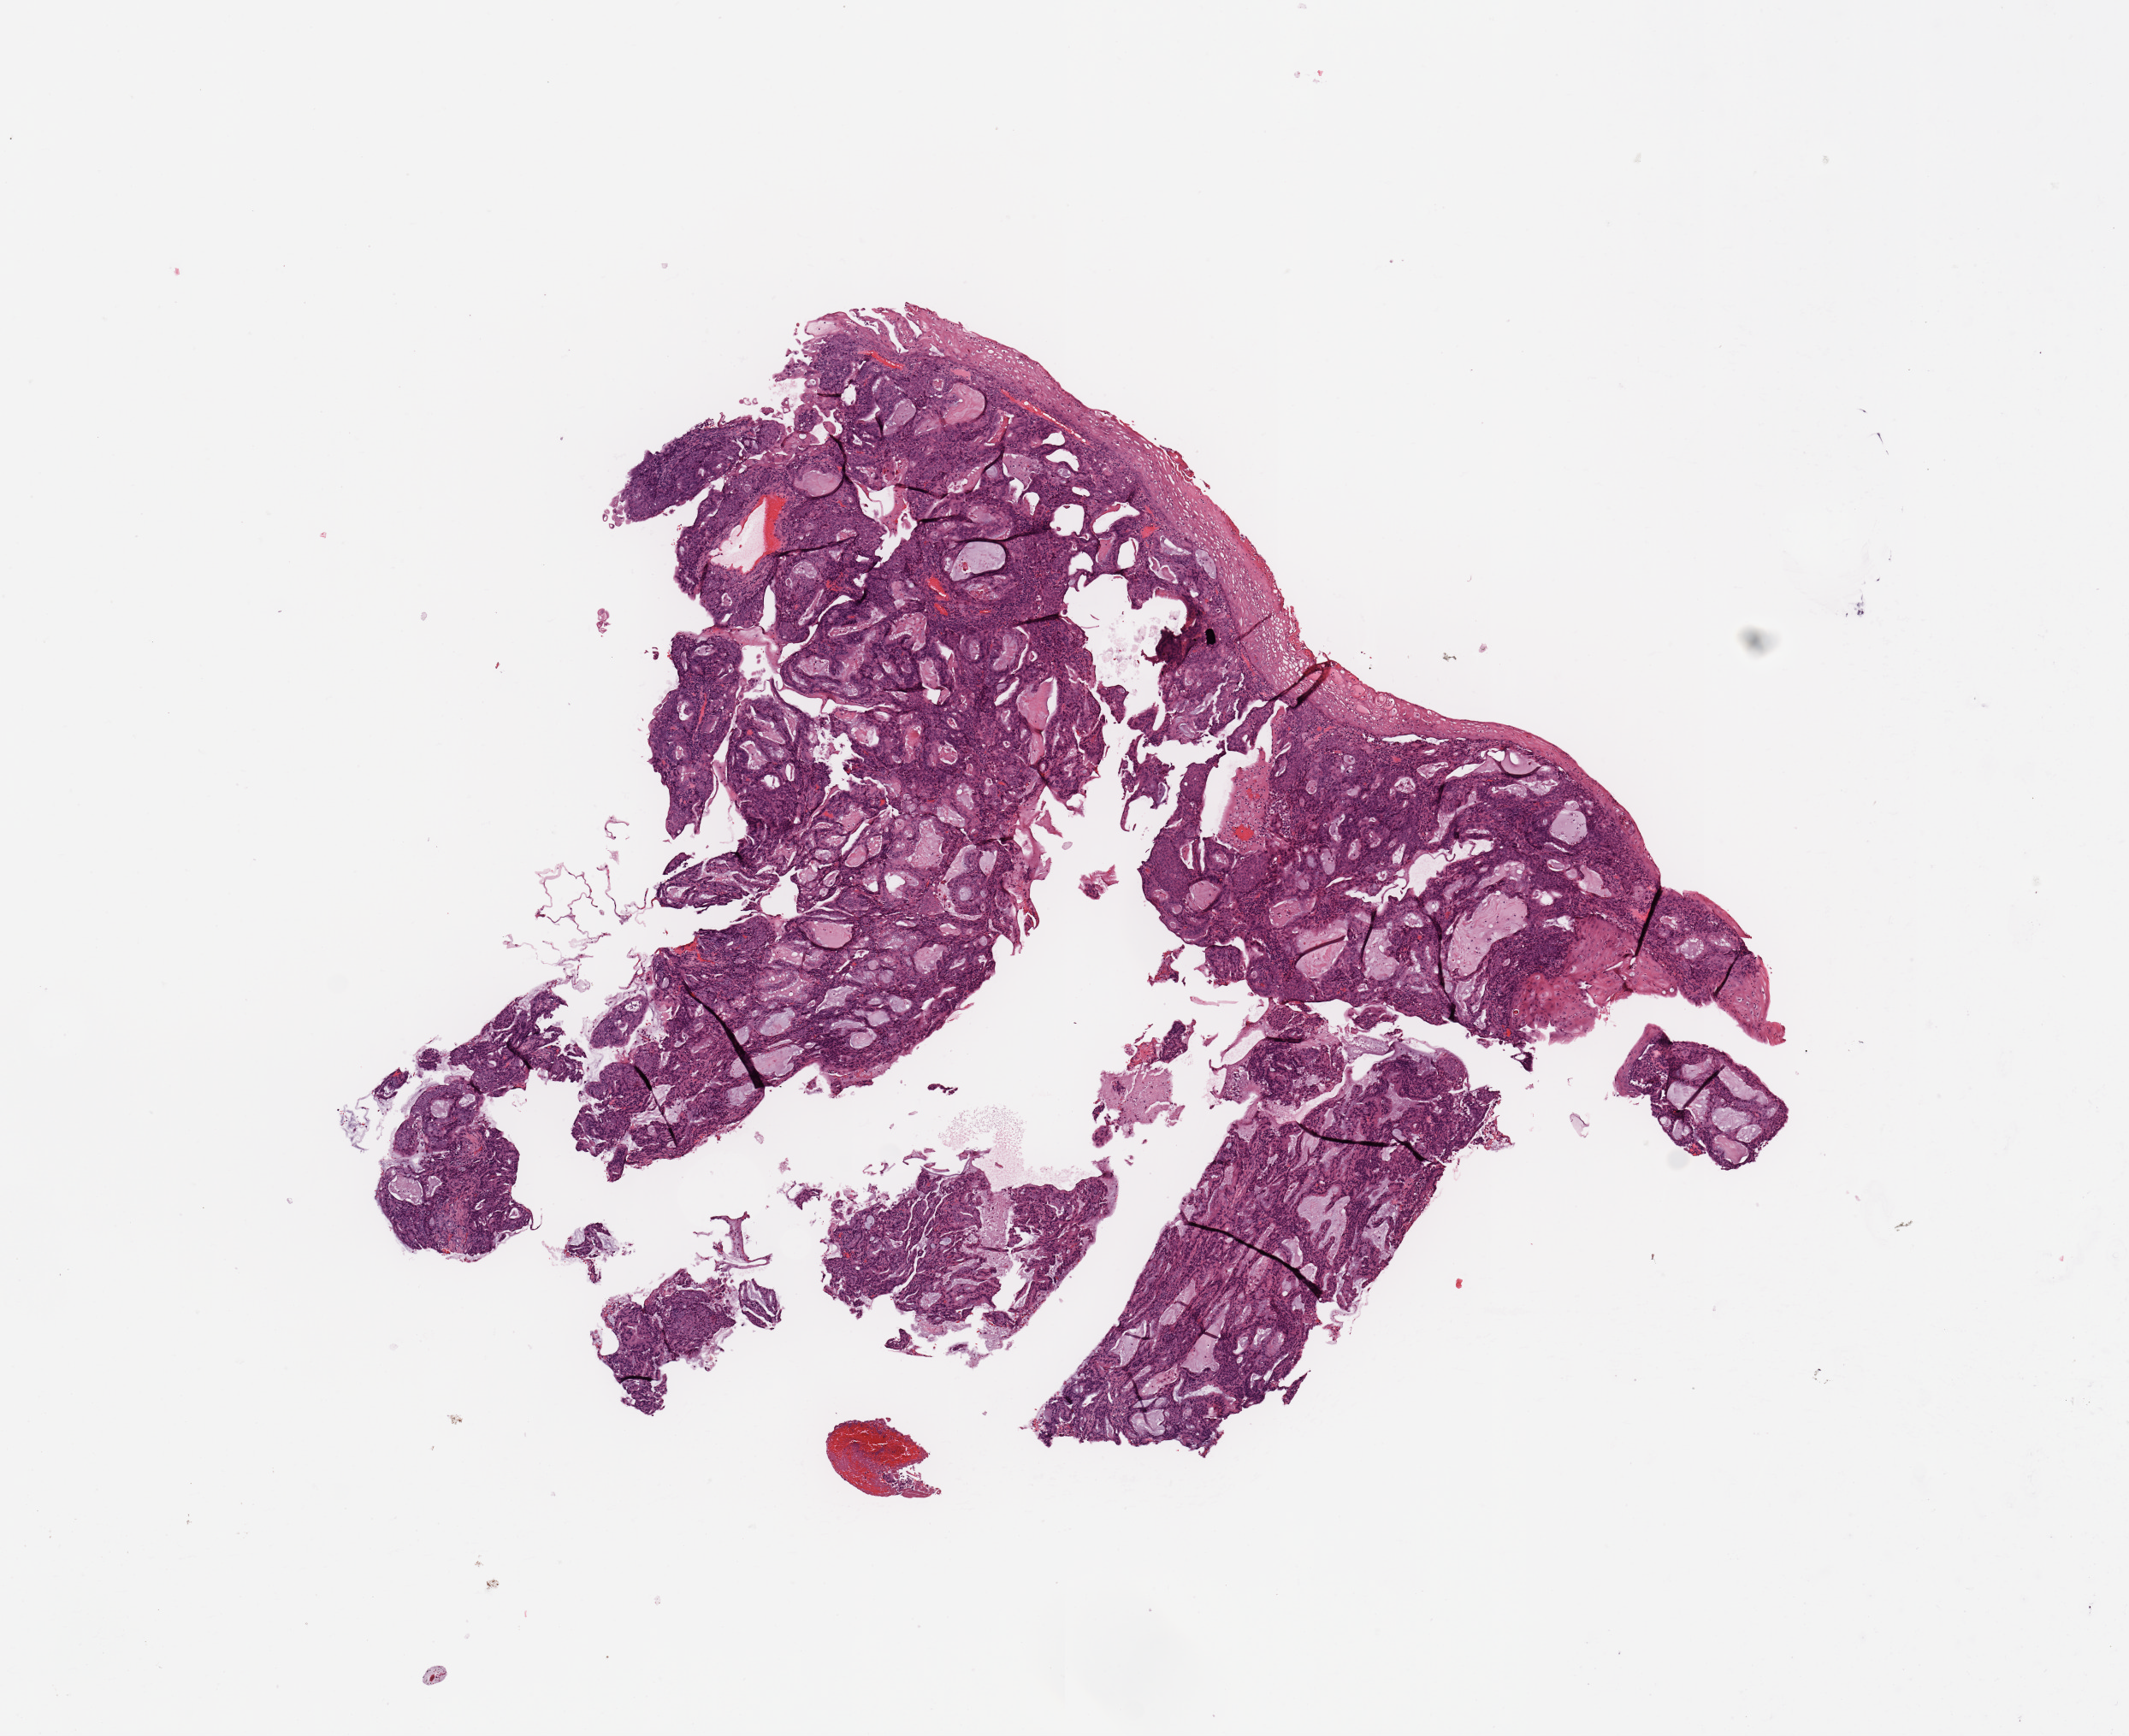
Hematoxylin and eosin (H&E) stained whole-slide image, shown as a low-resolution overview of the whole scanned area (about 9.8 x 8.0 mm); tumour tissue sample, uterus. Patient: female, age 54 years. Histologic grade: G2 (moderately differentiated).
AJCC pathologic stage: IIIB. Histologic diagnosis: Endometrioid adenocarcinoma, NOS.